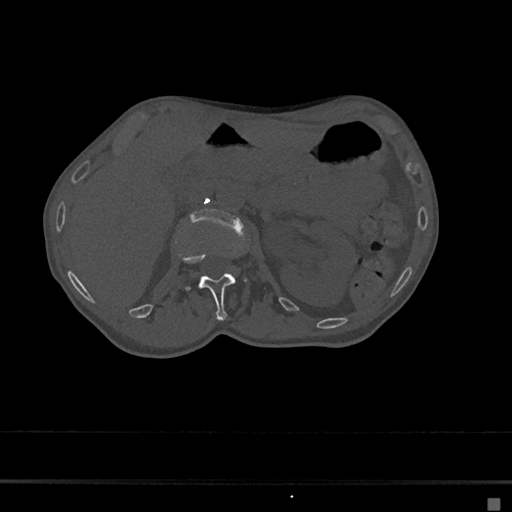
CT including the spine, one axial slice. Slice 58 of 797 in the series (ordered by position). 120 kVp. Bone window (W 1800 / L 400 HU). 0.5 mm slice thickness. 512 × 512 image matrix, field of view 360 × 360 mm. Female patient, age 68 years. Case-level facts recorded for this patient, not image findings: primary cancer: renal.
Annotated regions visible in this slice (semi-automatic segmentation, software-assisted and operator-edited):
- L1 vertebra: box from (x=177, y=251) to (x=248, y=320) px
- L2 vertebra: (x=190, y=208)–(x=241, y=228)